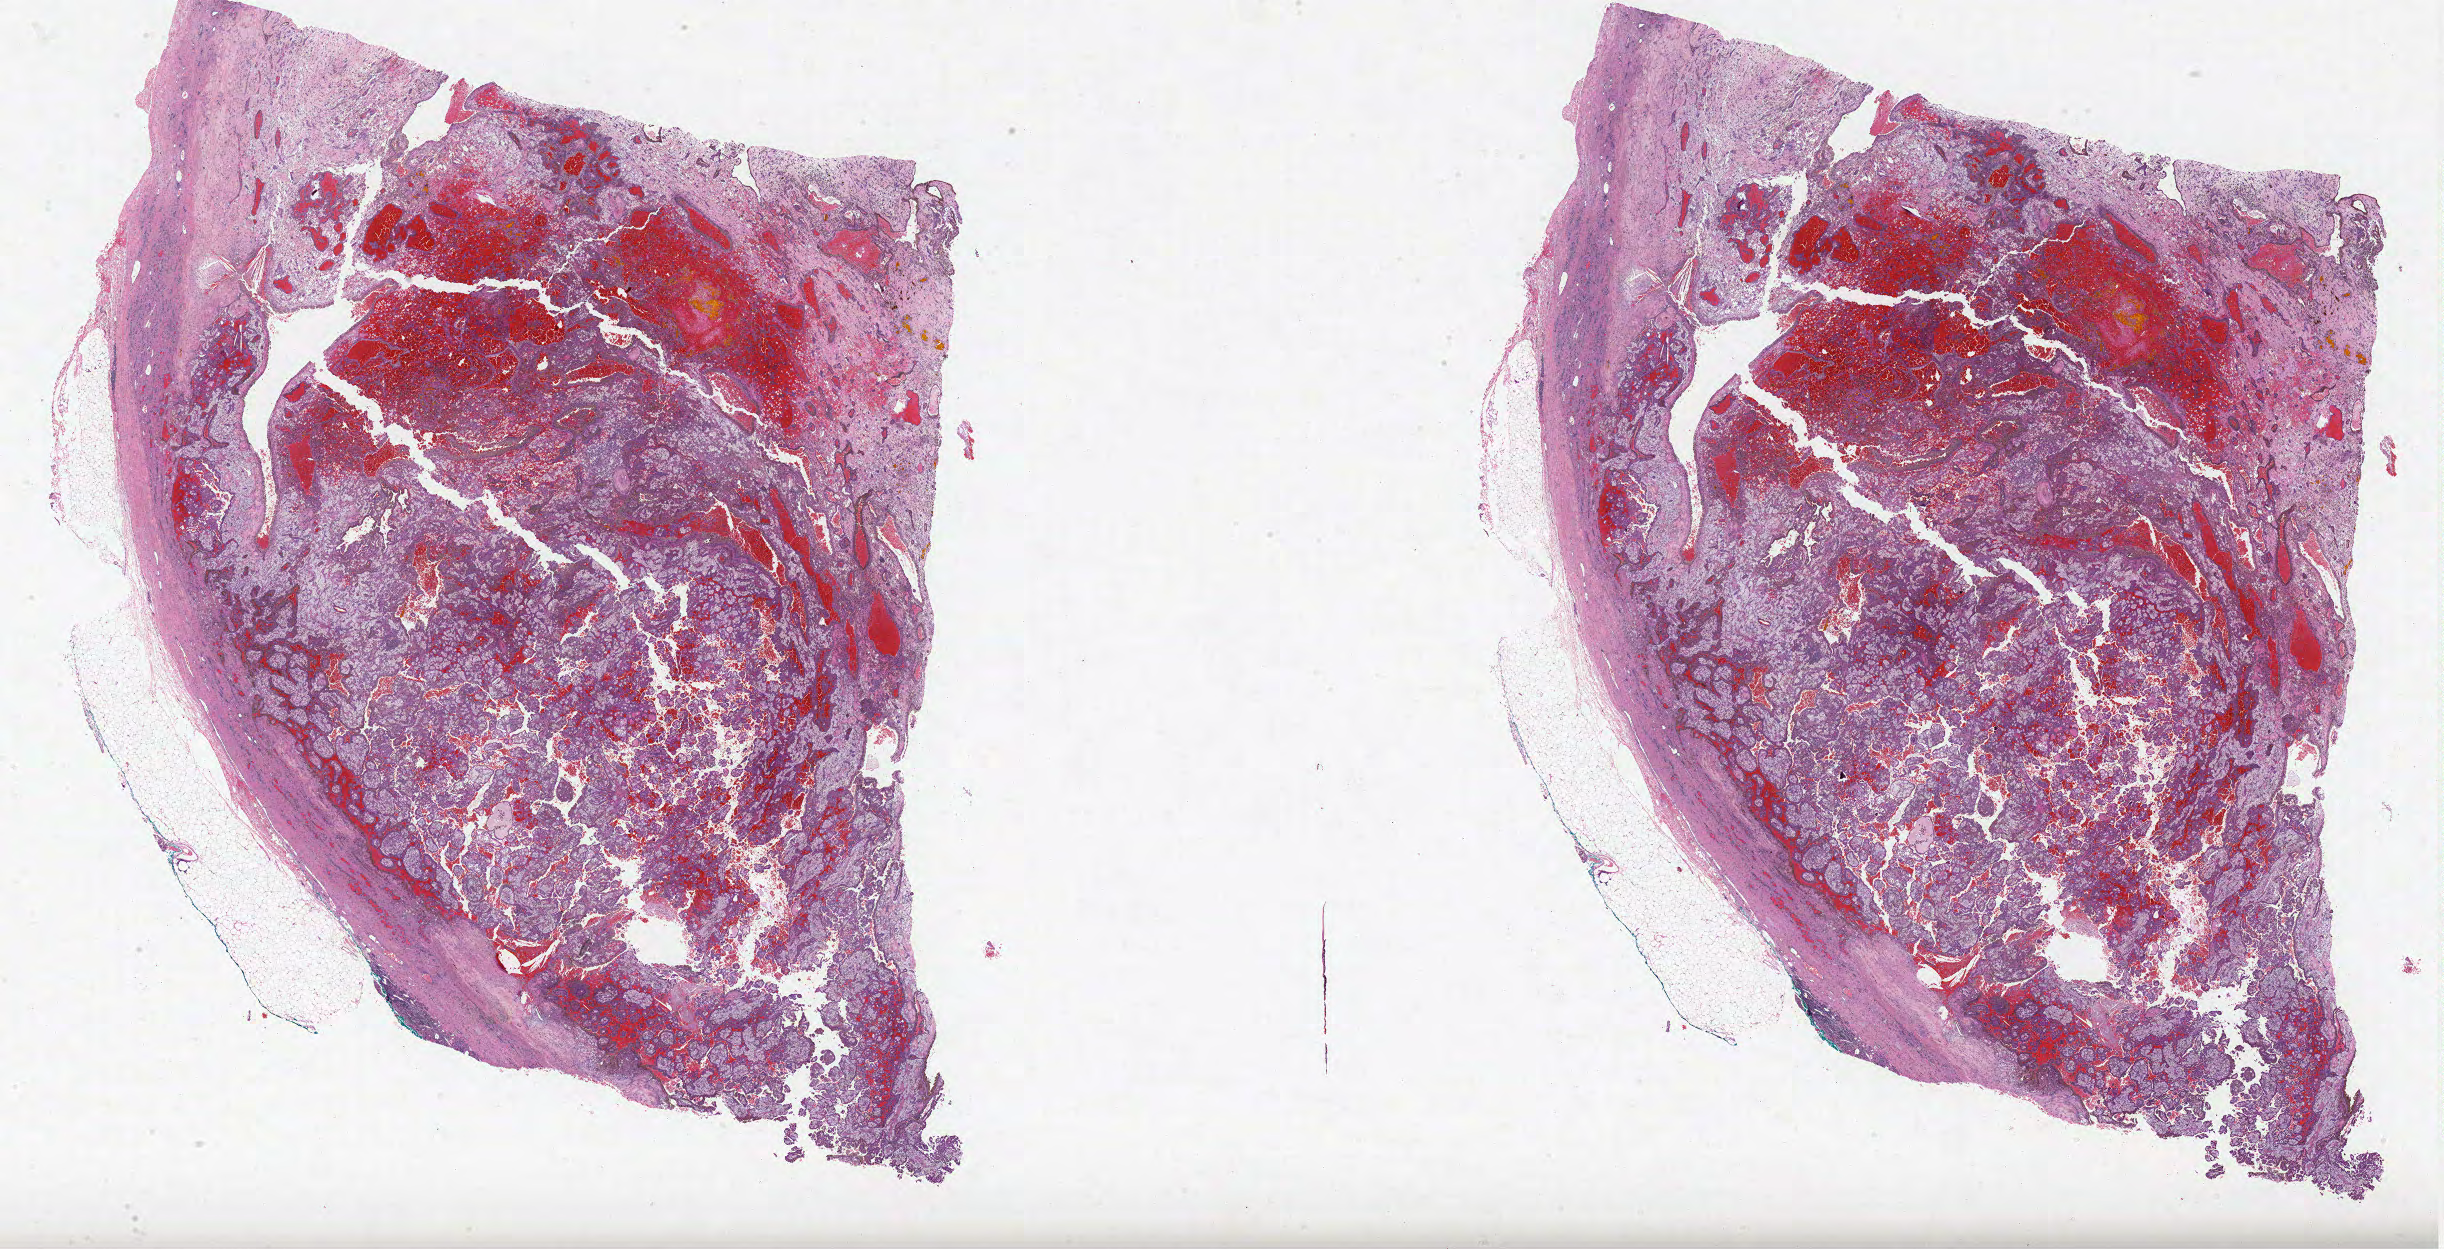
Digitized Hematoxylin and eosin (H&E) stained tissue section (whole slide) — whole scanned area (about 39.1 x 20.0 mm) shown as a low-resolution overview; FFPE section; primary tumour sample from the kidney. Male, age 71 years at initial diagnosis.
* AJCC pathologic stage: I (7th edition)
* TNM: T1b NX M0
* laterality: right
* diagnosis: Papillary adenocarcinoma, NOS